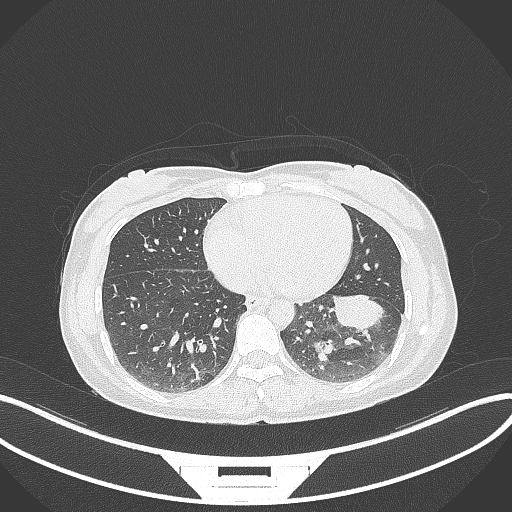
Chest CT, one axial slice; slice 16 of 244 in the series (ordered by position); reconstruction kernel B70f; 120 kVp; lung window (W 1500 / L -600 HU); 512 × 512 image matrix, field of view 400 × 400 mm. Female patient, age 41 years. Case-level facts recorded for this patient, not image findings: clinical TNM (as recorded): T2a N3 M1b.
Outlined on this slice (rectangle marked by the reading radiologist):
- lung tumour (recorded histology: adenocarcinoma): box from (x=326, y=286) to (x=389, y=336) px